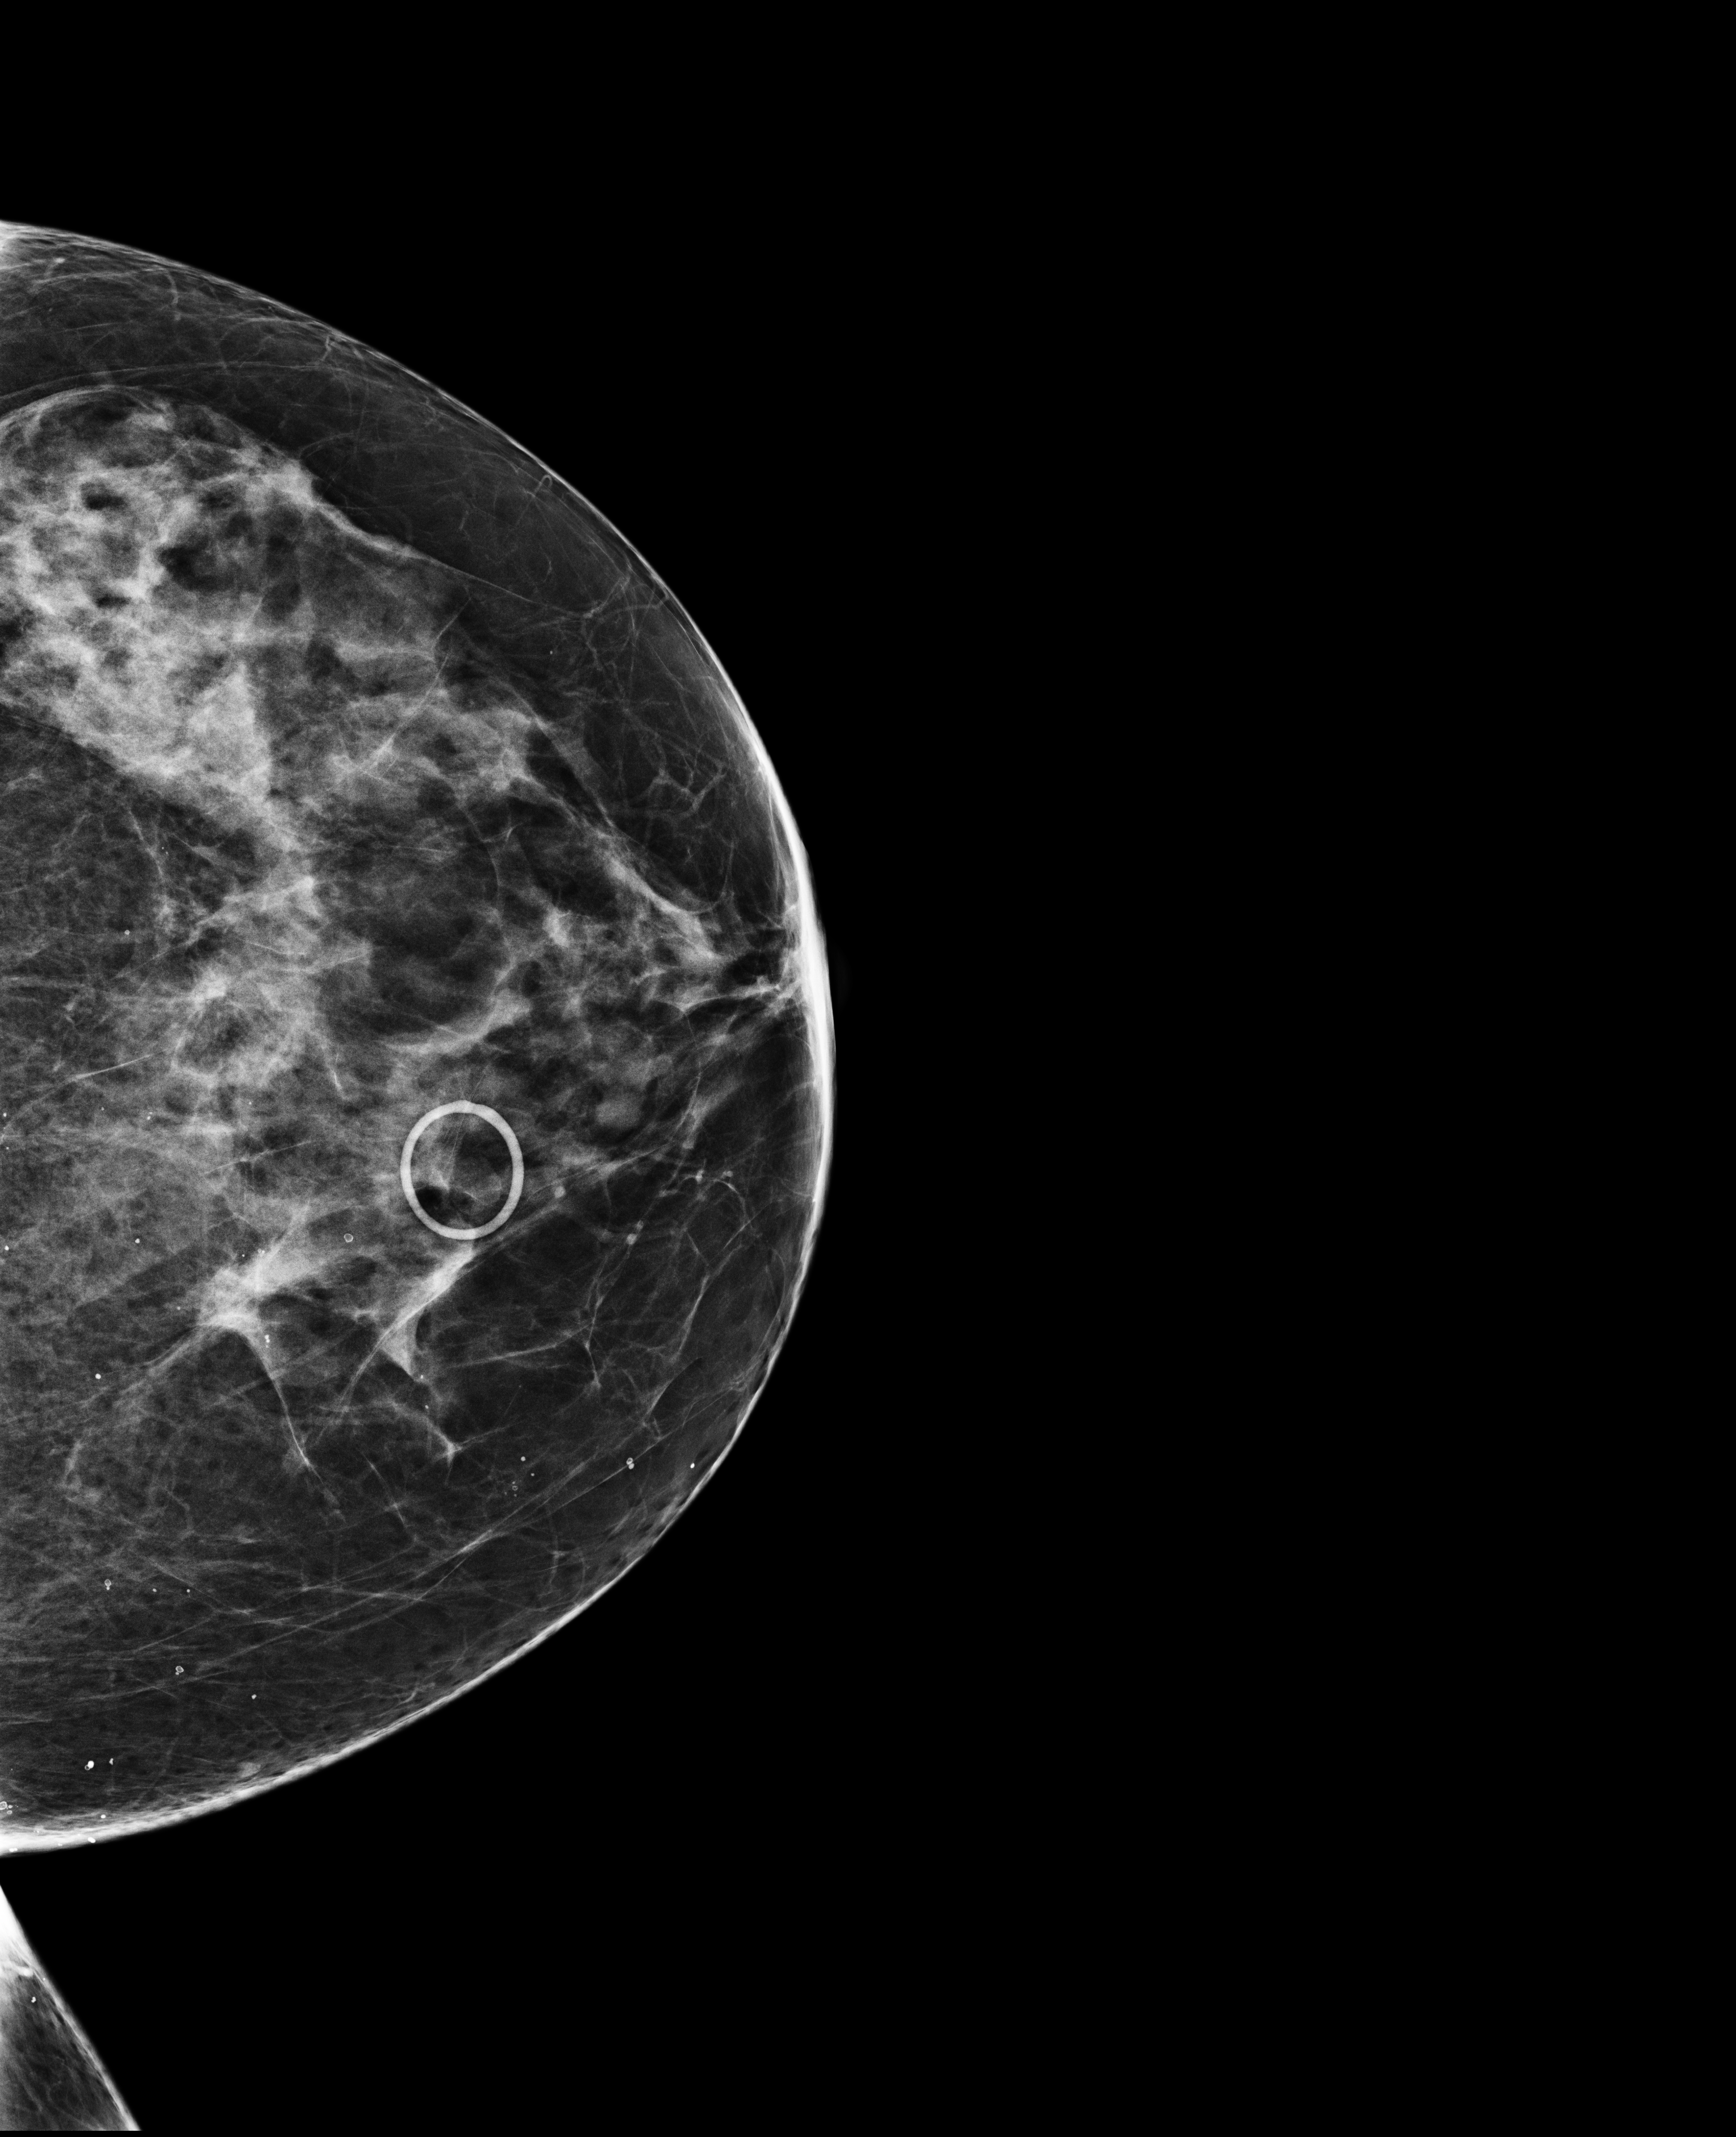
Digital mammogram (FFDM), left breast, craniocaudal (CC) view, annual screening mammography examination. Patient: female, 60 years.
BI-RADS breast density category at the screening exam (both breasts, scale 1–4): 3. Final BI-RADS assessment for this screening round (tomosynthesis exam, both breasts): category 1. Recall: recalled for additional imaging after this screen.